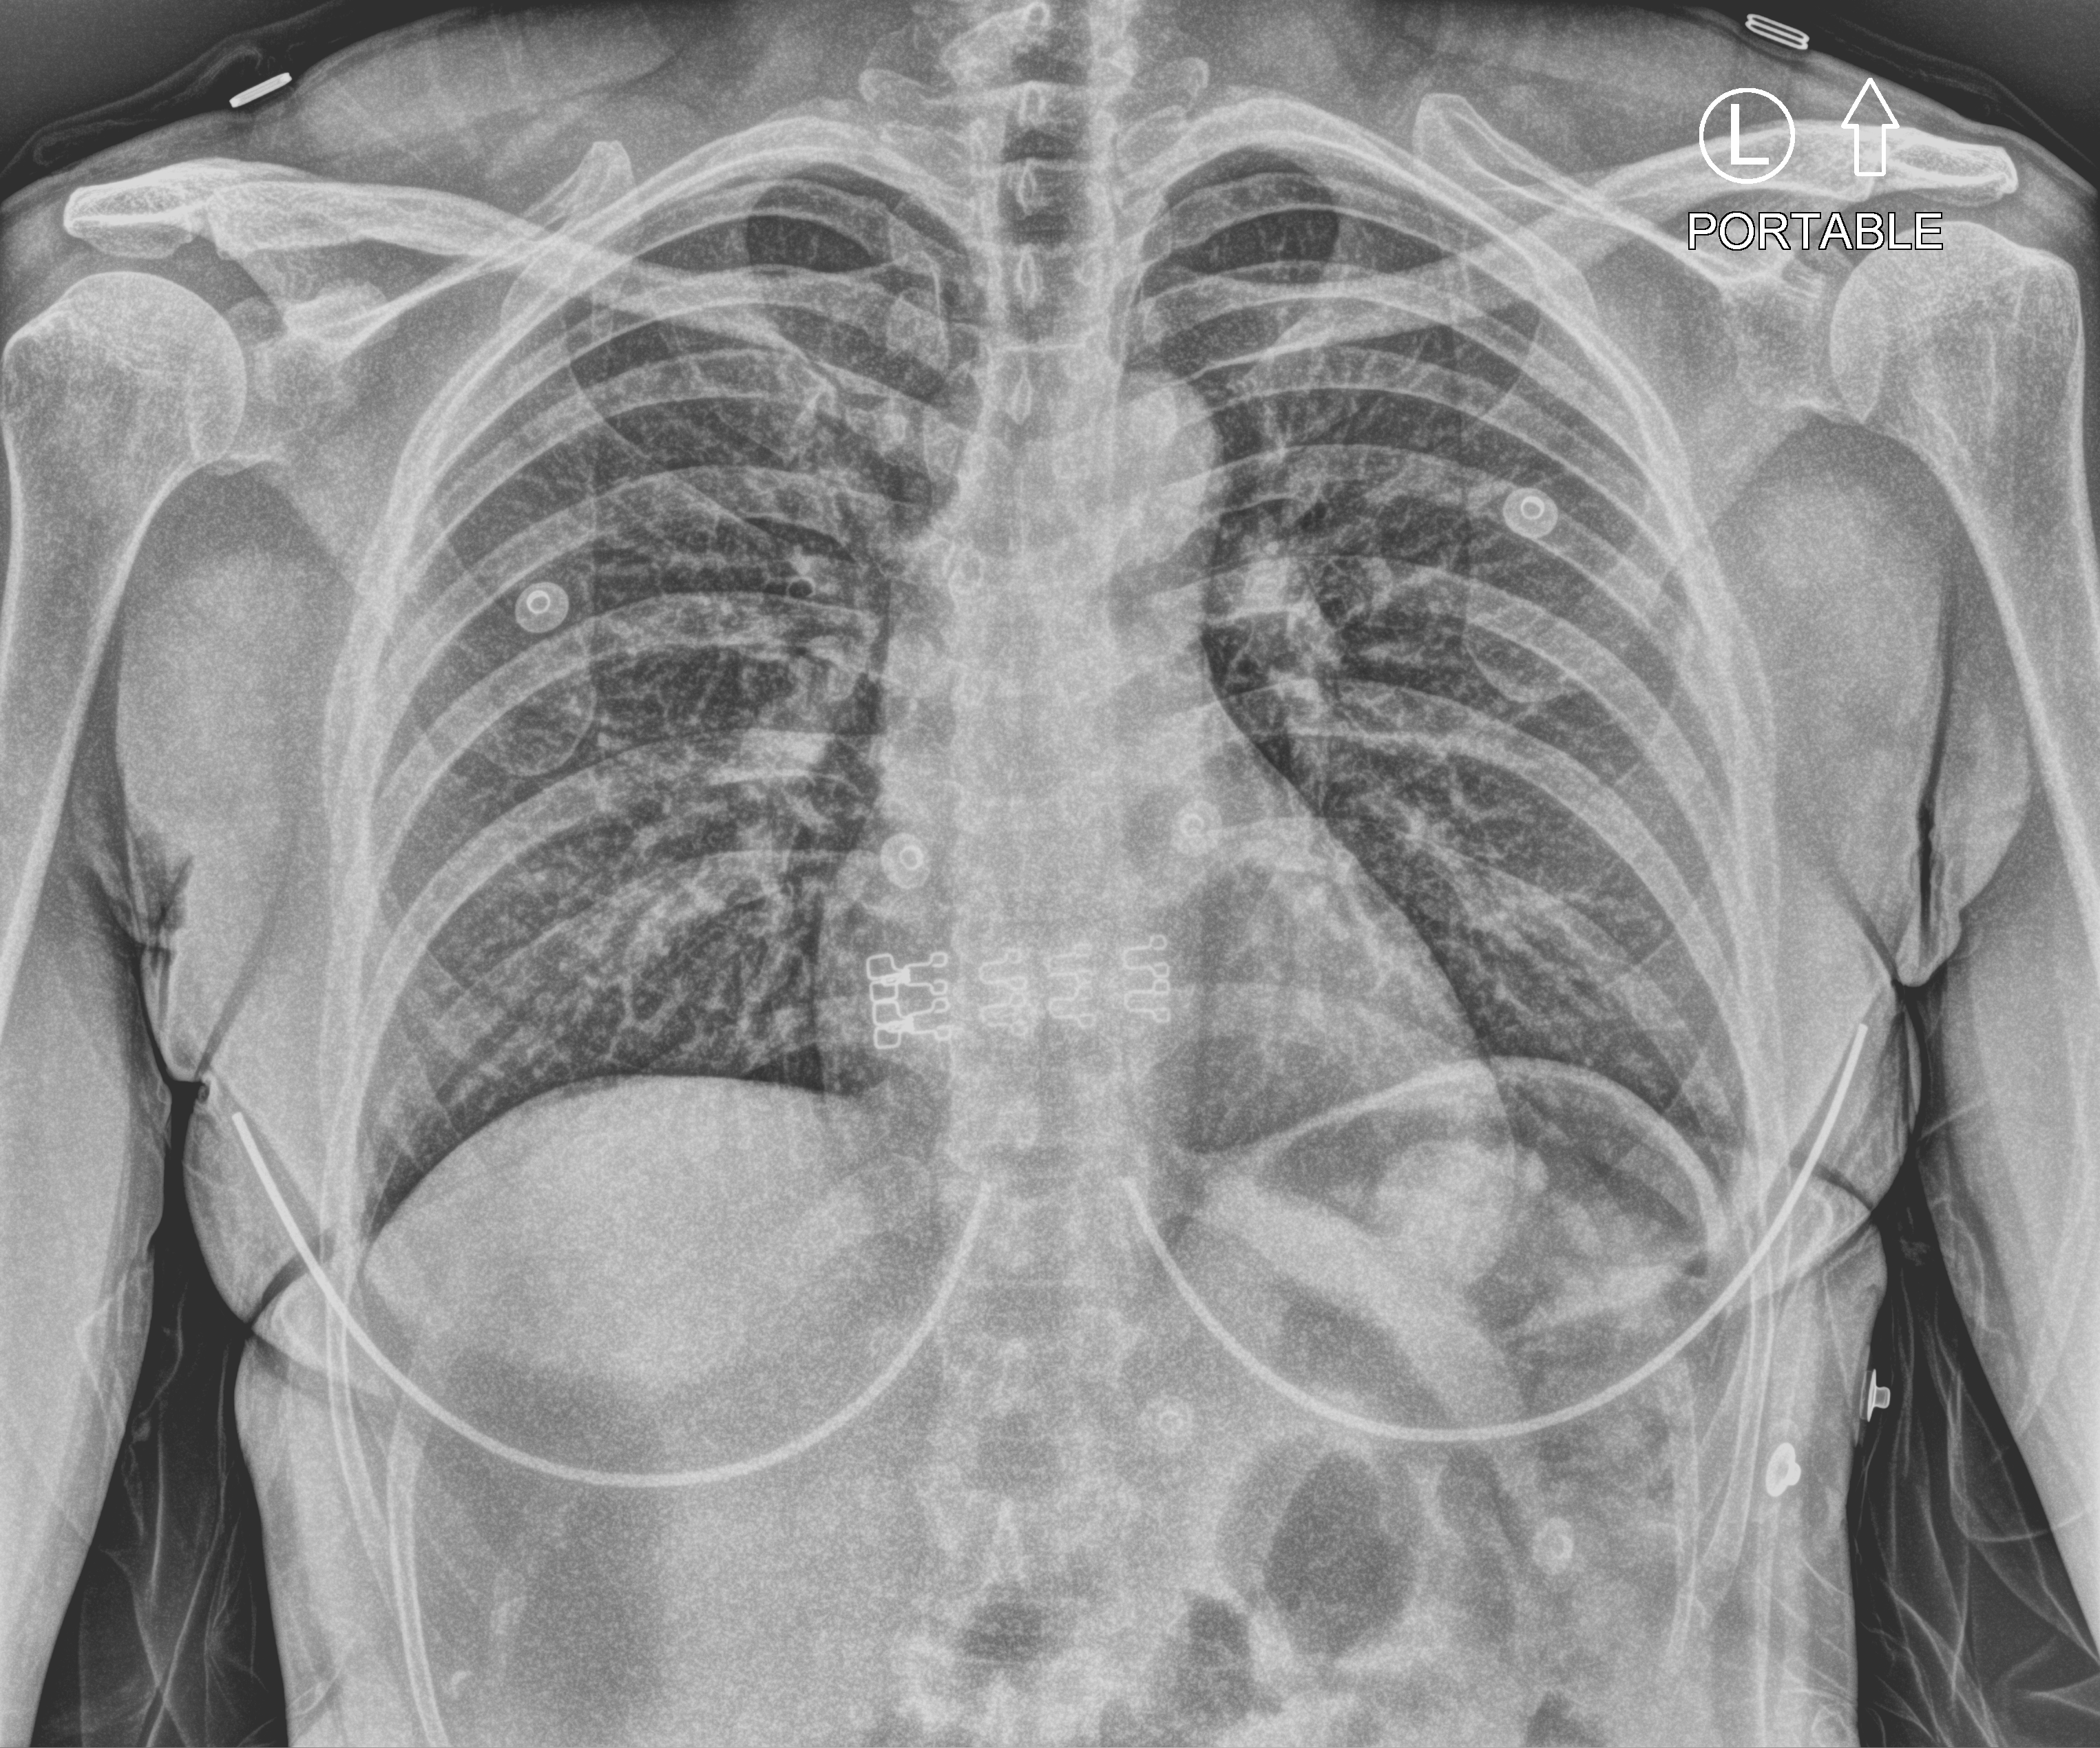
Bedside chest radiograph (computed radiography), anteroposterior (AP) projection. Female patient hospitalised with COVID-19, age 18–59 years.
From the hospital-stay record, not from the radiograph (when in the stay this image was taken is not recorded):
- admitted to intensive care during this hospital stay: no
- length of hospital stay: 1 day